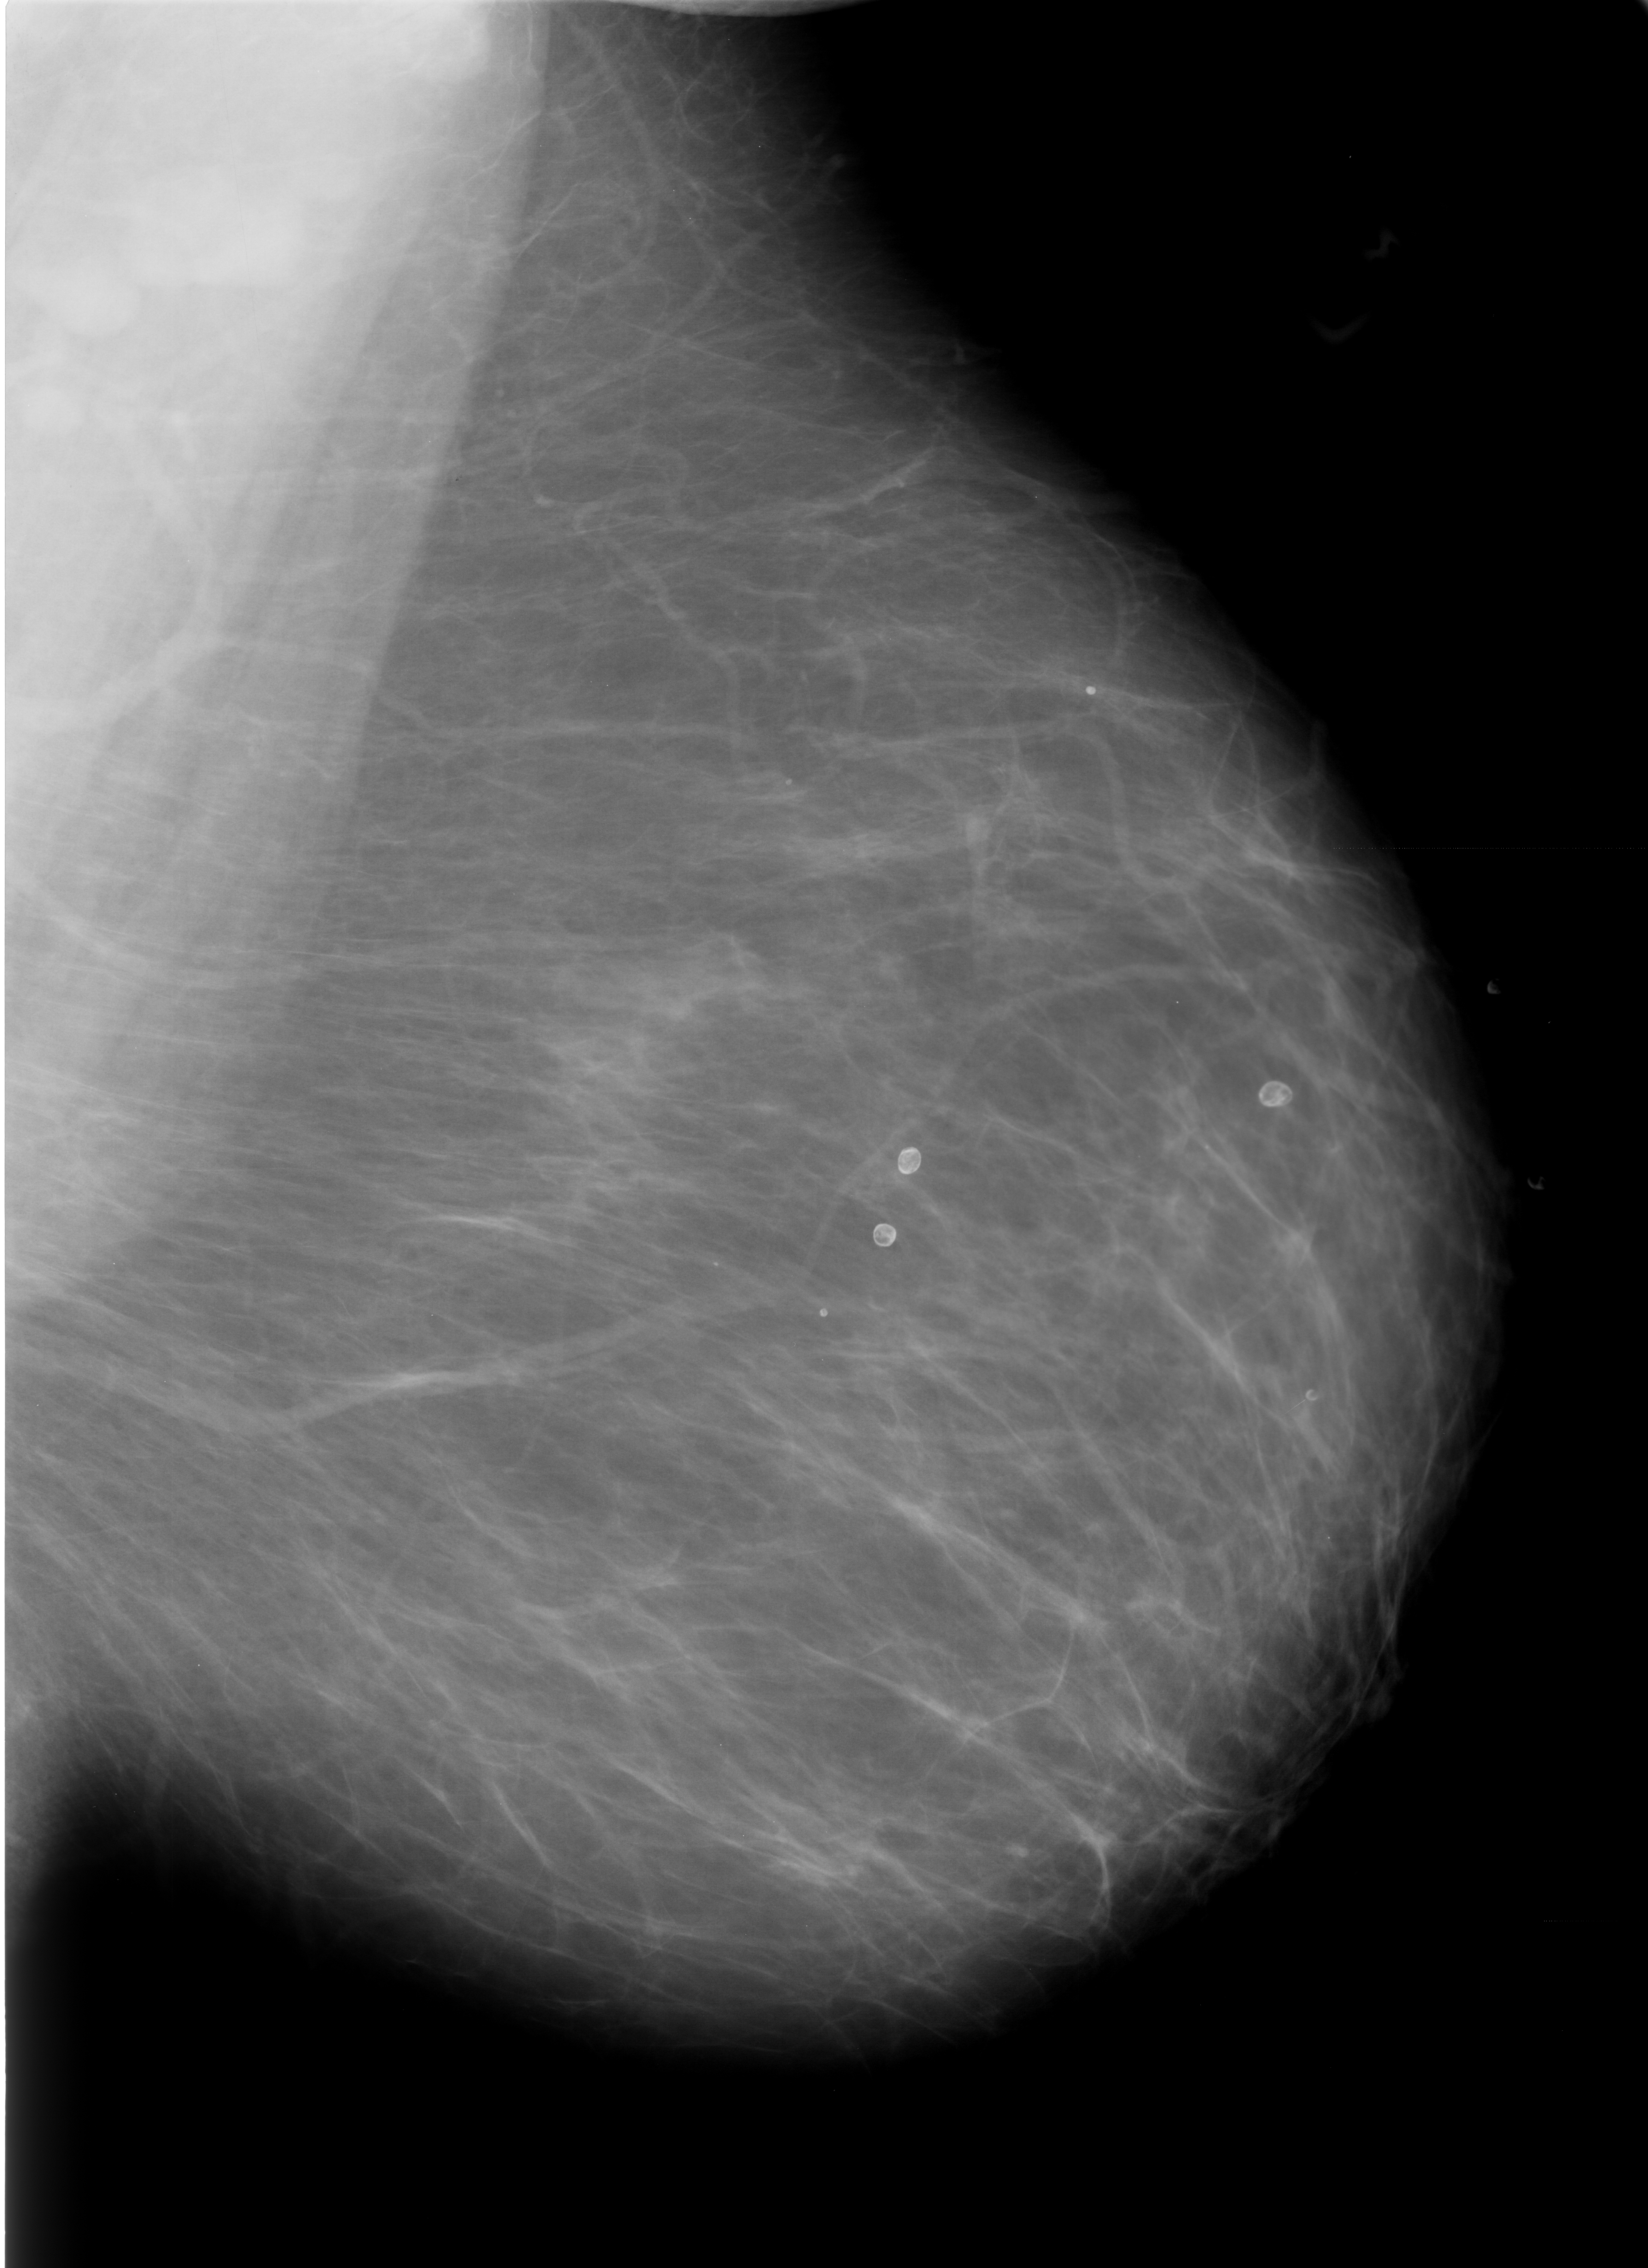
Scanned film-screen mammogram. Left breast. MLO view. BI-RADS breast density category 1 (scale 1–4). 1648 × 2268 image matrix.
Marked abnormalities (boxes around the expert regions of interest):
- Finding 1 of 7: calcifications, morphology lucent center; BI-RADS assessment category 2; subtlety rating 5 on a 1 (subtle) to 5 (obvious) scale; outcome (as recorded, no biopsy): benign without callback (not worked up further): box from (x=804, y=1297) to (x=835, y=1334) px
- Finding 2 of 7: calcifications, morphology lucent center; BI-RADS assessment category 2; subtlety rating 5 on a 1 (subtle) to 5 (obvious) scale; outcome (as recorded, no biopsy): benign without callback (not worked up further): (x=859, y=1210)–(x=903, y=1263)
- Finding 3 of 7: calcifications, morphology lucent center; BI-RADS assessment category 2; outcome (as recorded, no biopsy): benign without callback (not worked up further): (x=879, y=1142)–(x=929, y=1185)
- Finding 4 of 7: calcifications, morphology lucent center; BI-RADS assessment category 2; subtlety rating 5 on a 1 (subtle) to 5 (obvious) scale; outcome (as recorded, no biopsy): benign without callback (not worked up further): (x=1070, y=678)–(x=1107, y=705)
- Finding 5 of 7: calcifications, morphology eggshell; BI-RADS assessment category 2; subtlety rating 5 on a 1 (subtle) to 5 (obvious) scale; benign; no additional work-up was recommended (outcome (as recorded, no biopsy): benign without callback): (x=1248, y=1070)–(x=1302, y=1117)
- Finding 6 of 7: calcifications, morphology lucent center; BI-RADS assessment category 2; subtlety rating 5 on a 1 (subtle) to 5 (obvious) scale; outcome (as recorded, no biopsy): benign without callback (not worked up further): (x=1469, y=973)–(x=1513, y=1013)
- Finding 7 of 7: calcifications, morphology lucent center; BI-RADS assessment category 2; benign; no additional work-up was recommended (outcome (as recorded, no biopsy): benign without callback): (x=1511, y=1161)–(x=1558, y=1201)